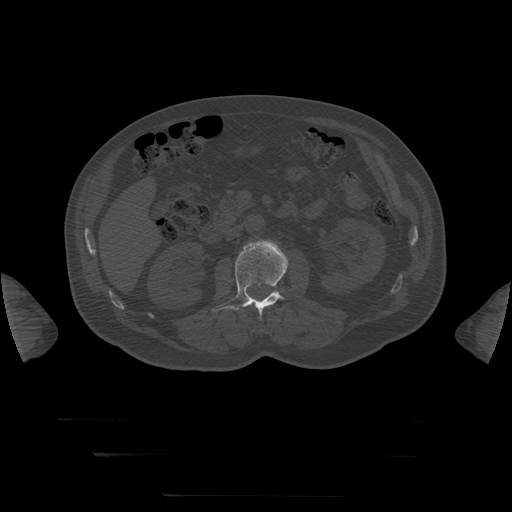
CT including the spine, one axial slice; position 22 of 397 along the scan axis; reconstruction kernel STANDARD; 120 kVp; bone window (W 1800 / L 400 HU); 512 × 512 image matrix, field of view 510 × 510 mm. Patient age 73 years. From the clinical record (not read from this slice): primary cancer: prostate.
Structures marked on this image (semi-automatic segmentation, software-assisted and operator-edited):
- L1 vertebra: box from (x=253, y=302) to (x=267, y=307) px